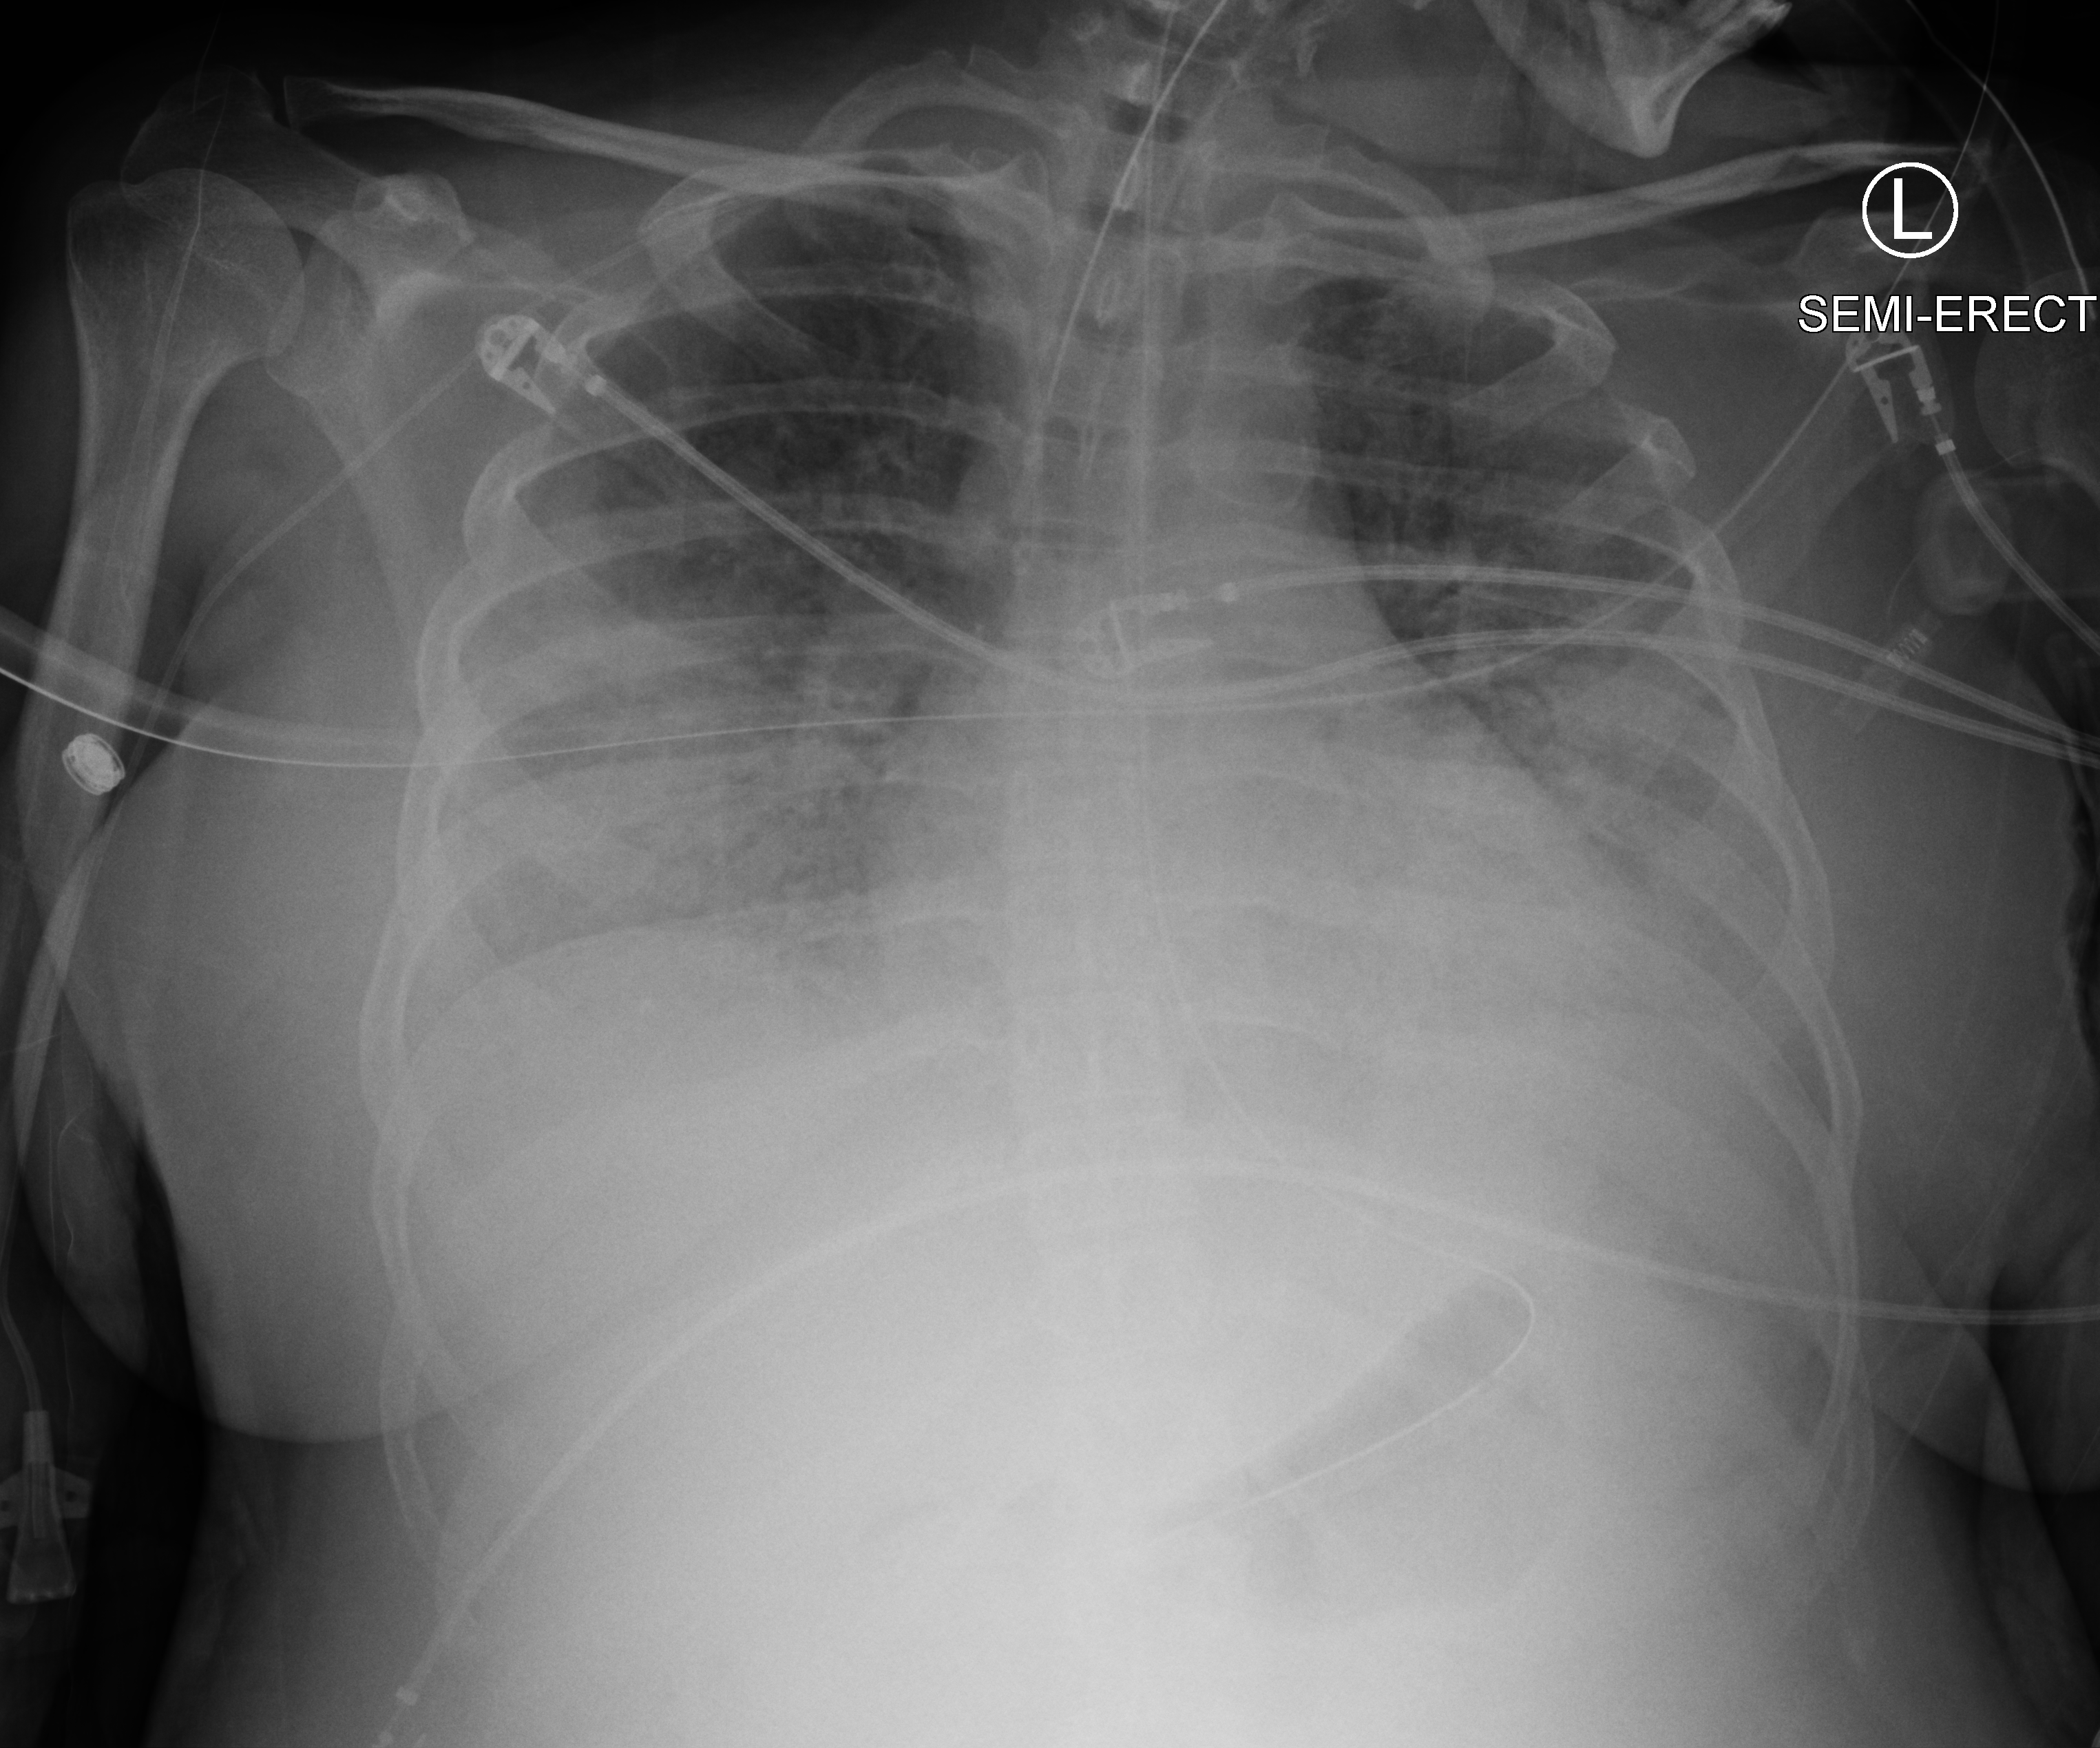
Portable chest radiograph; anteroposterior (AP) projection. Patient hospitalised with COVID-19, aged 18–59 years.
From the hospital-stay record, not from the radiograph (when in the stay this image was taken is not recorded): COPD (admission record): no; mechanically ventilated during this hospital stay: yes; admitted to intensive care during this hospital stay: yes.